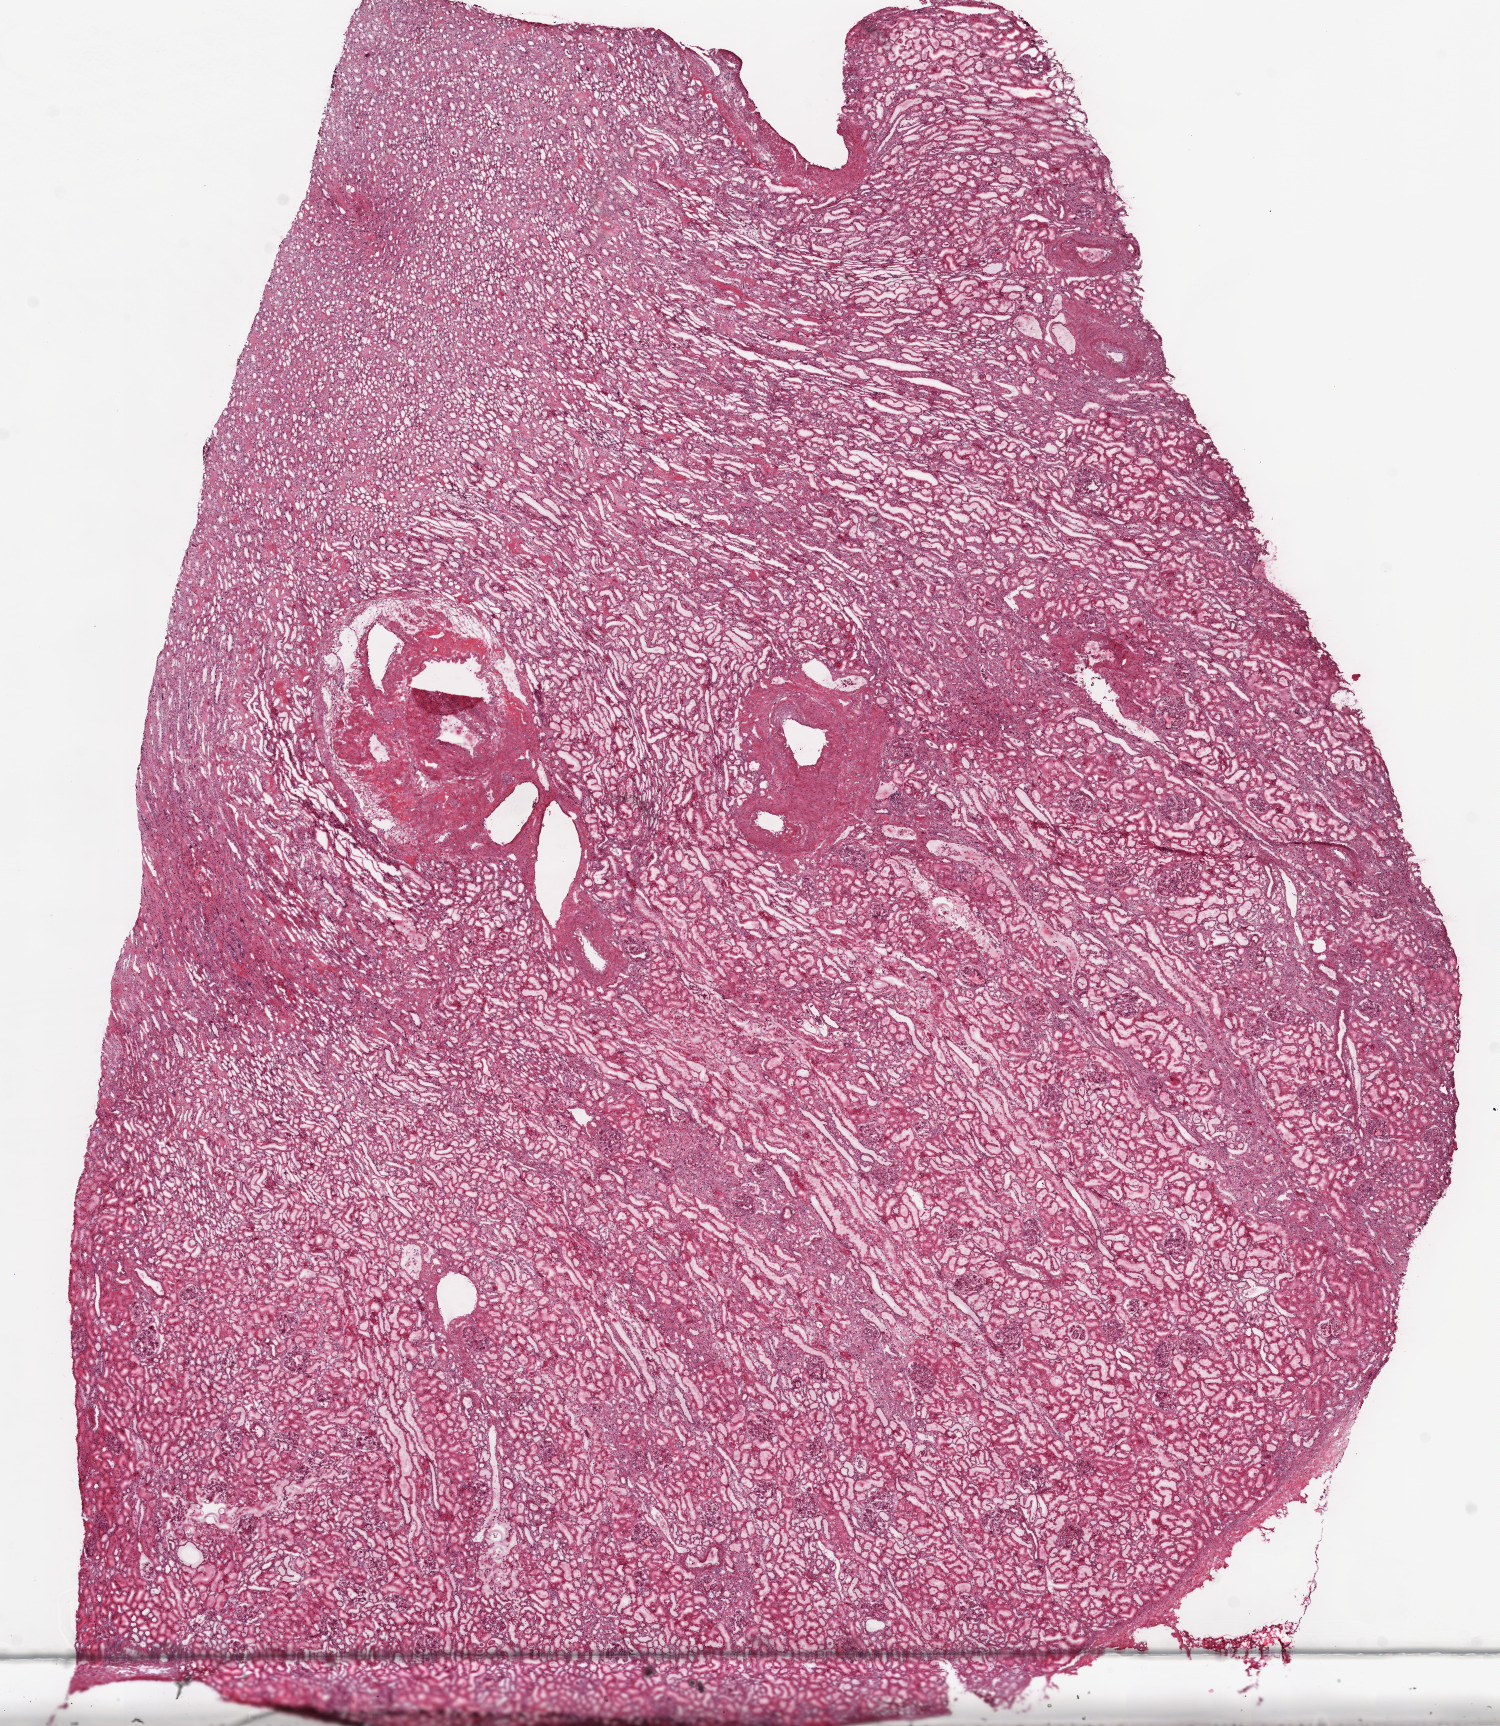
Whole-slide histology image, Hematoxylin and eosin (H&E) stained — whole scanned area (about 12.0 x 13.9 mm, slide scanned at 20x) shown as a low-resolution overview; frozen section from the top of the tissue portion; sample: solid tissue normal (non-tumour tissue), kidney. Patient: male, age at initial diagnosis 71 years.
This section: solid tissue normal (non-tumour) sample from the same patient. Patient diagnosis: Clear cell adenocarcinoma, NOS.